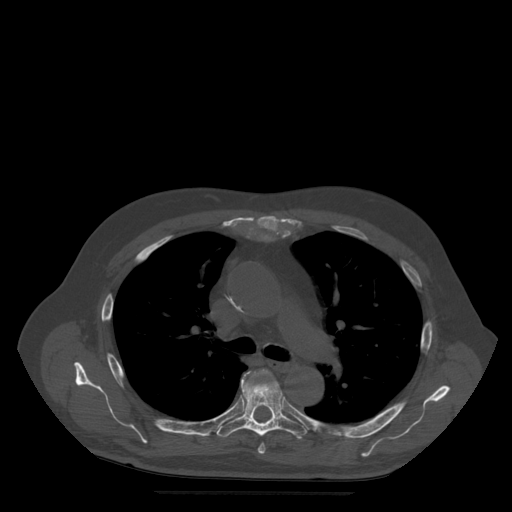
CT including the spine, one axial slice. Position 358 of 522 along the scan axis. Bone window (W 1800 / L 400 HU). 1.25 mm slice thickness. 512 × 512 image matrix, field of view 420 × 420 mm. Patient age 72 years. From the clinical record (not read from this slice): primary cancer: prostate.
Structures marked on this image (semi-automatically segmented with operator editing):
- T5 vertebra: bounding box [x1, y1, x2, y2] px = [248, 370, 266, 454]
- T6 vertebra: [217, 371, 307, 439]